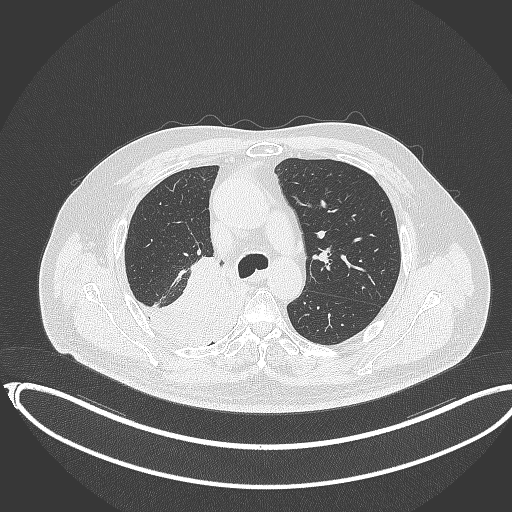
Chest CT, one axial slice; slice 243 of 403 in the series (ordered by position); reconstruction kernel B70f; 120 kVp; lung window (W 1500 / L -600 HU); 1 mm slice thickness; 512 × 512 image matrix, field of view 436 × 436 mm. Patient: male, 68 years. Case-level facts recorded for this patient, not image findings: clinical TNM (as recorded): T2a N0 M0.
Outlined on this slice (bounding box drawn by a radiologist):
- lung tumour (recorded histology: adenocarcinoma): box from (x=124, y=254) to (x=249, y=357) px